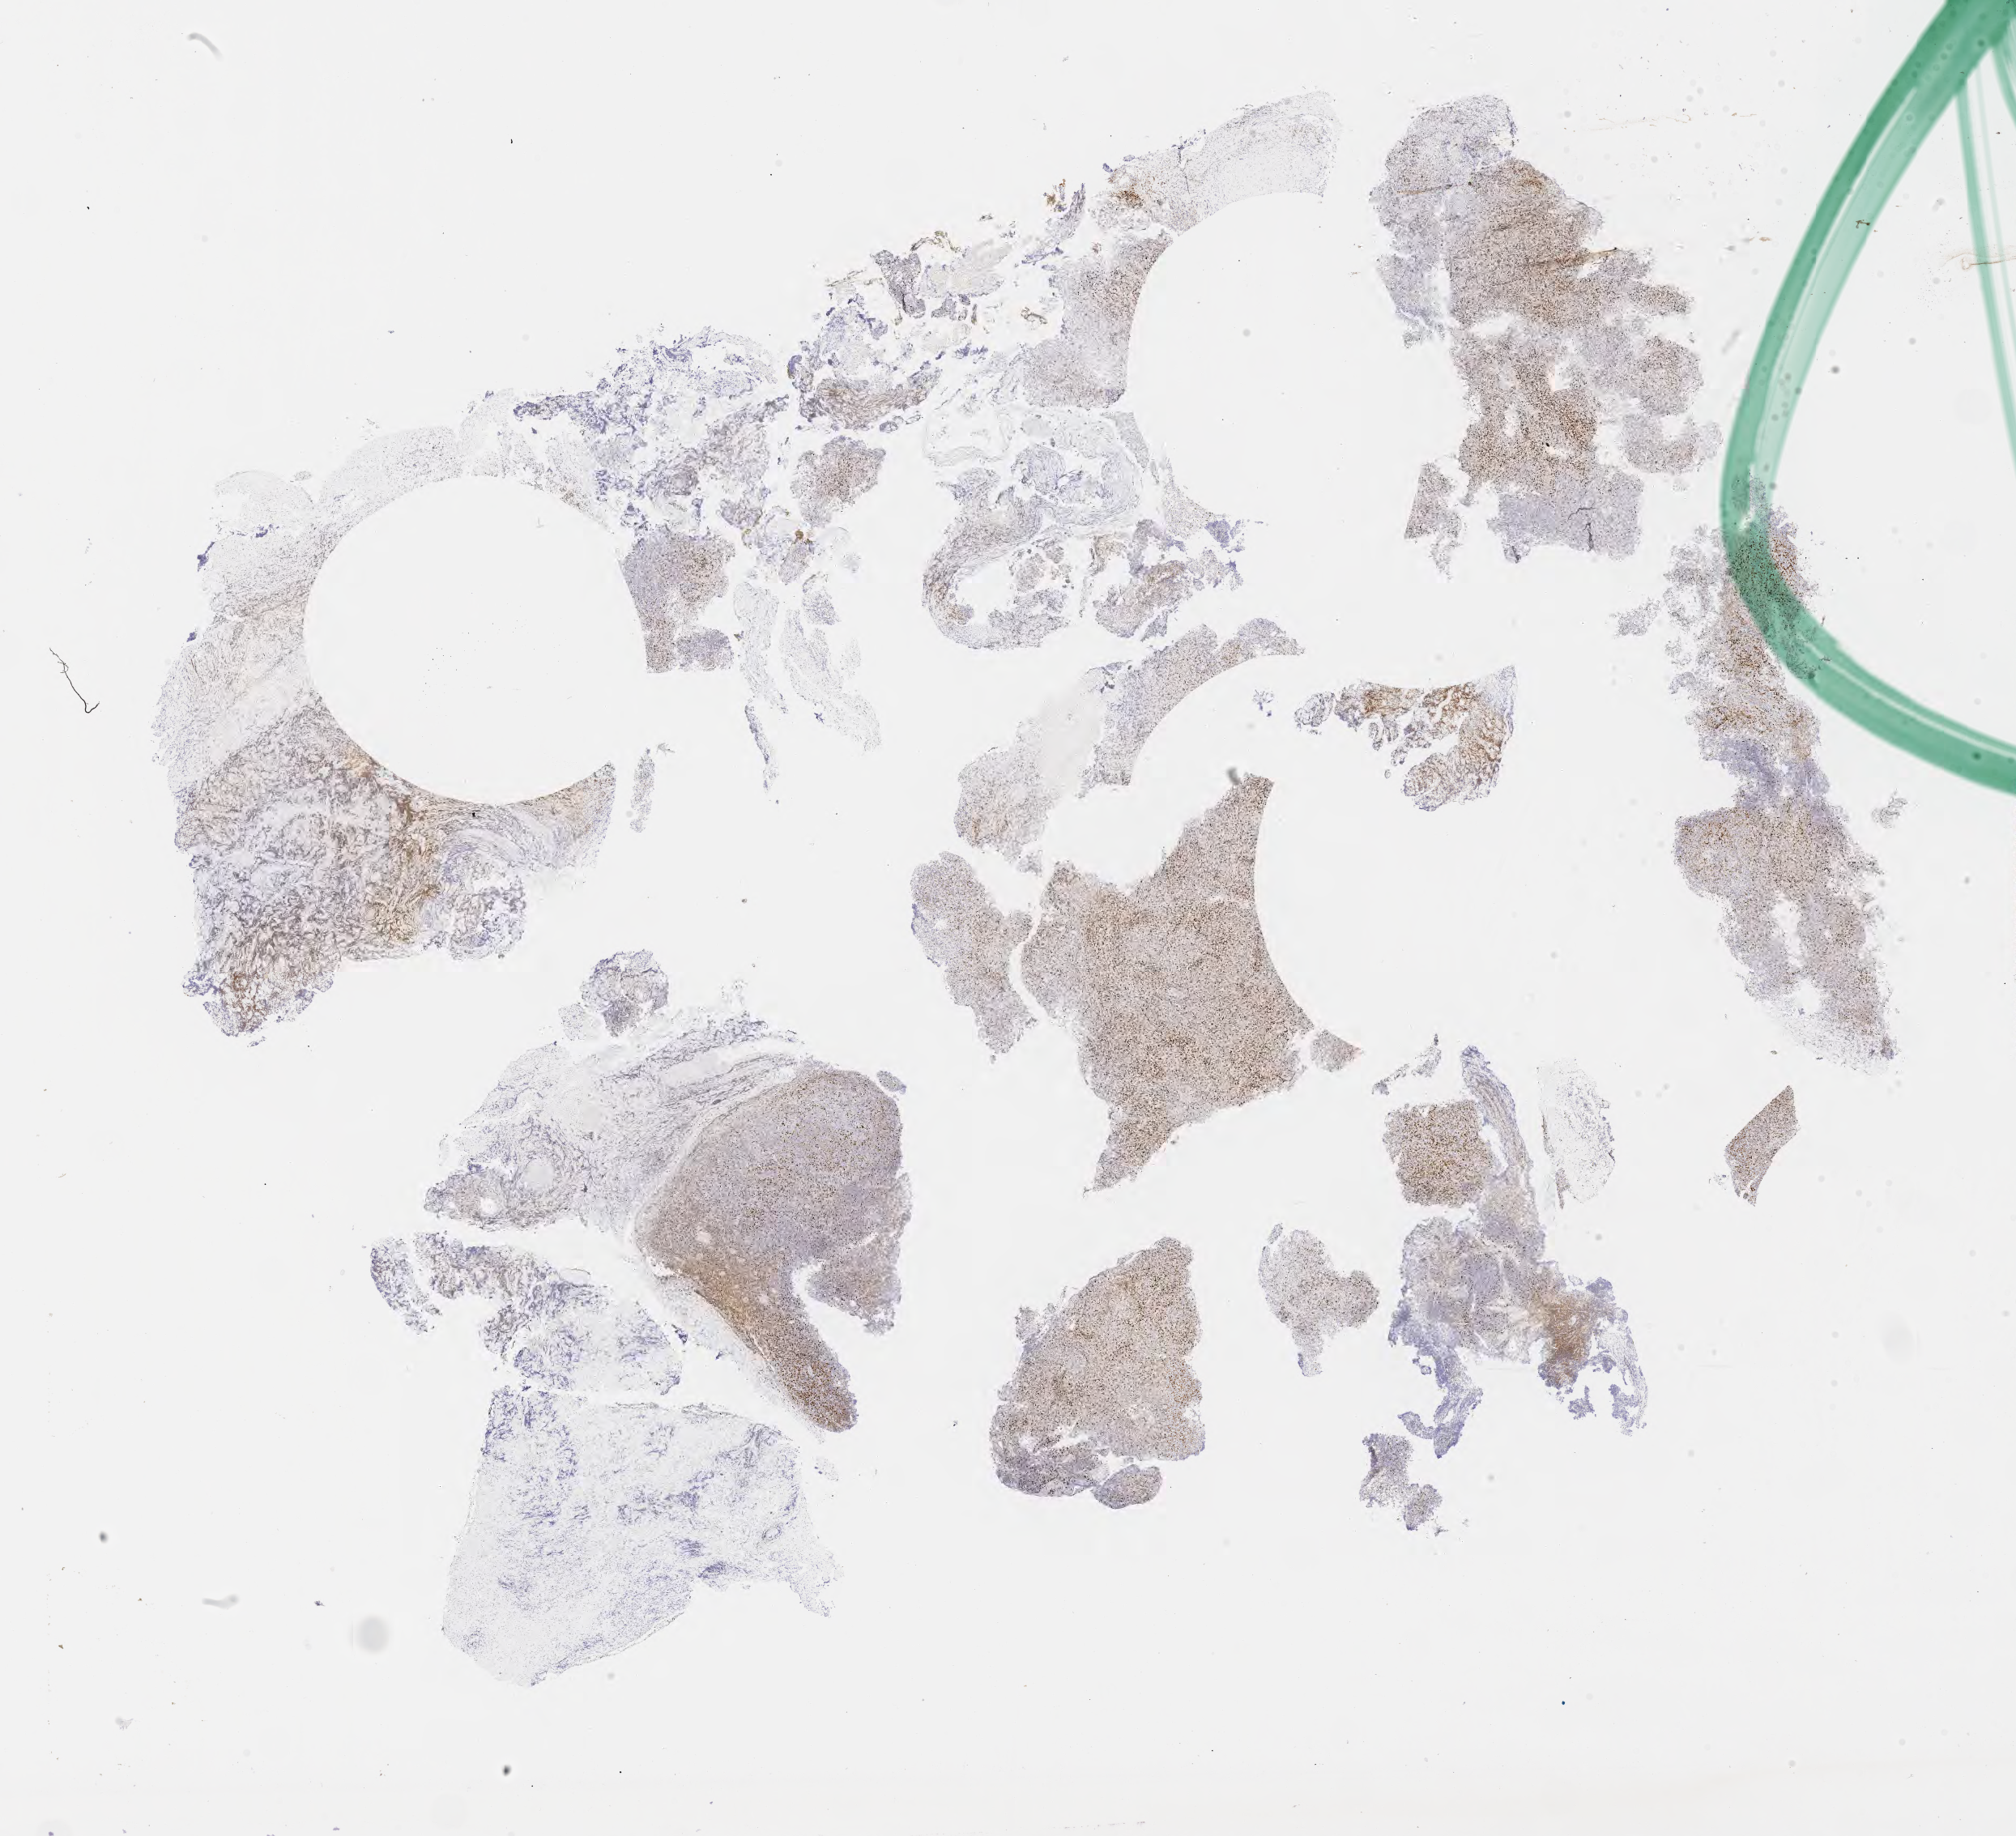
IHC for IRF4/MUM1, whole-slide image, low-resolution overview of the scanned area, about 20.1 x 18.3 mm. Tumor tissue. Site: lymph node. Patient male; 29 years old.
Diagnosis: Diffuse large B-cell lymphoma, NOS.